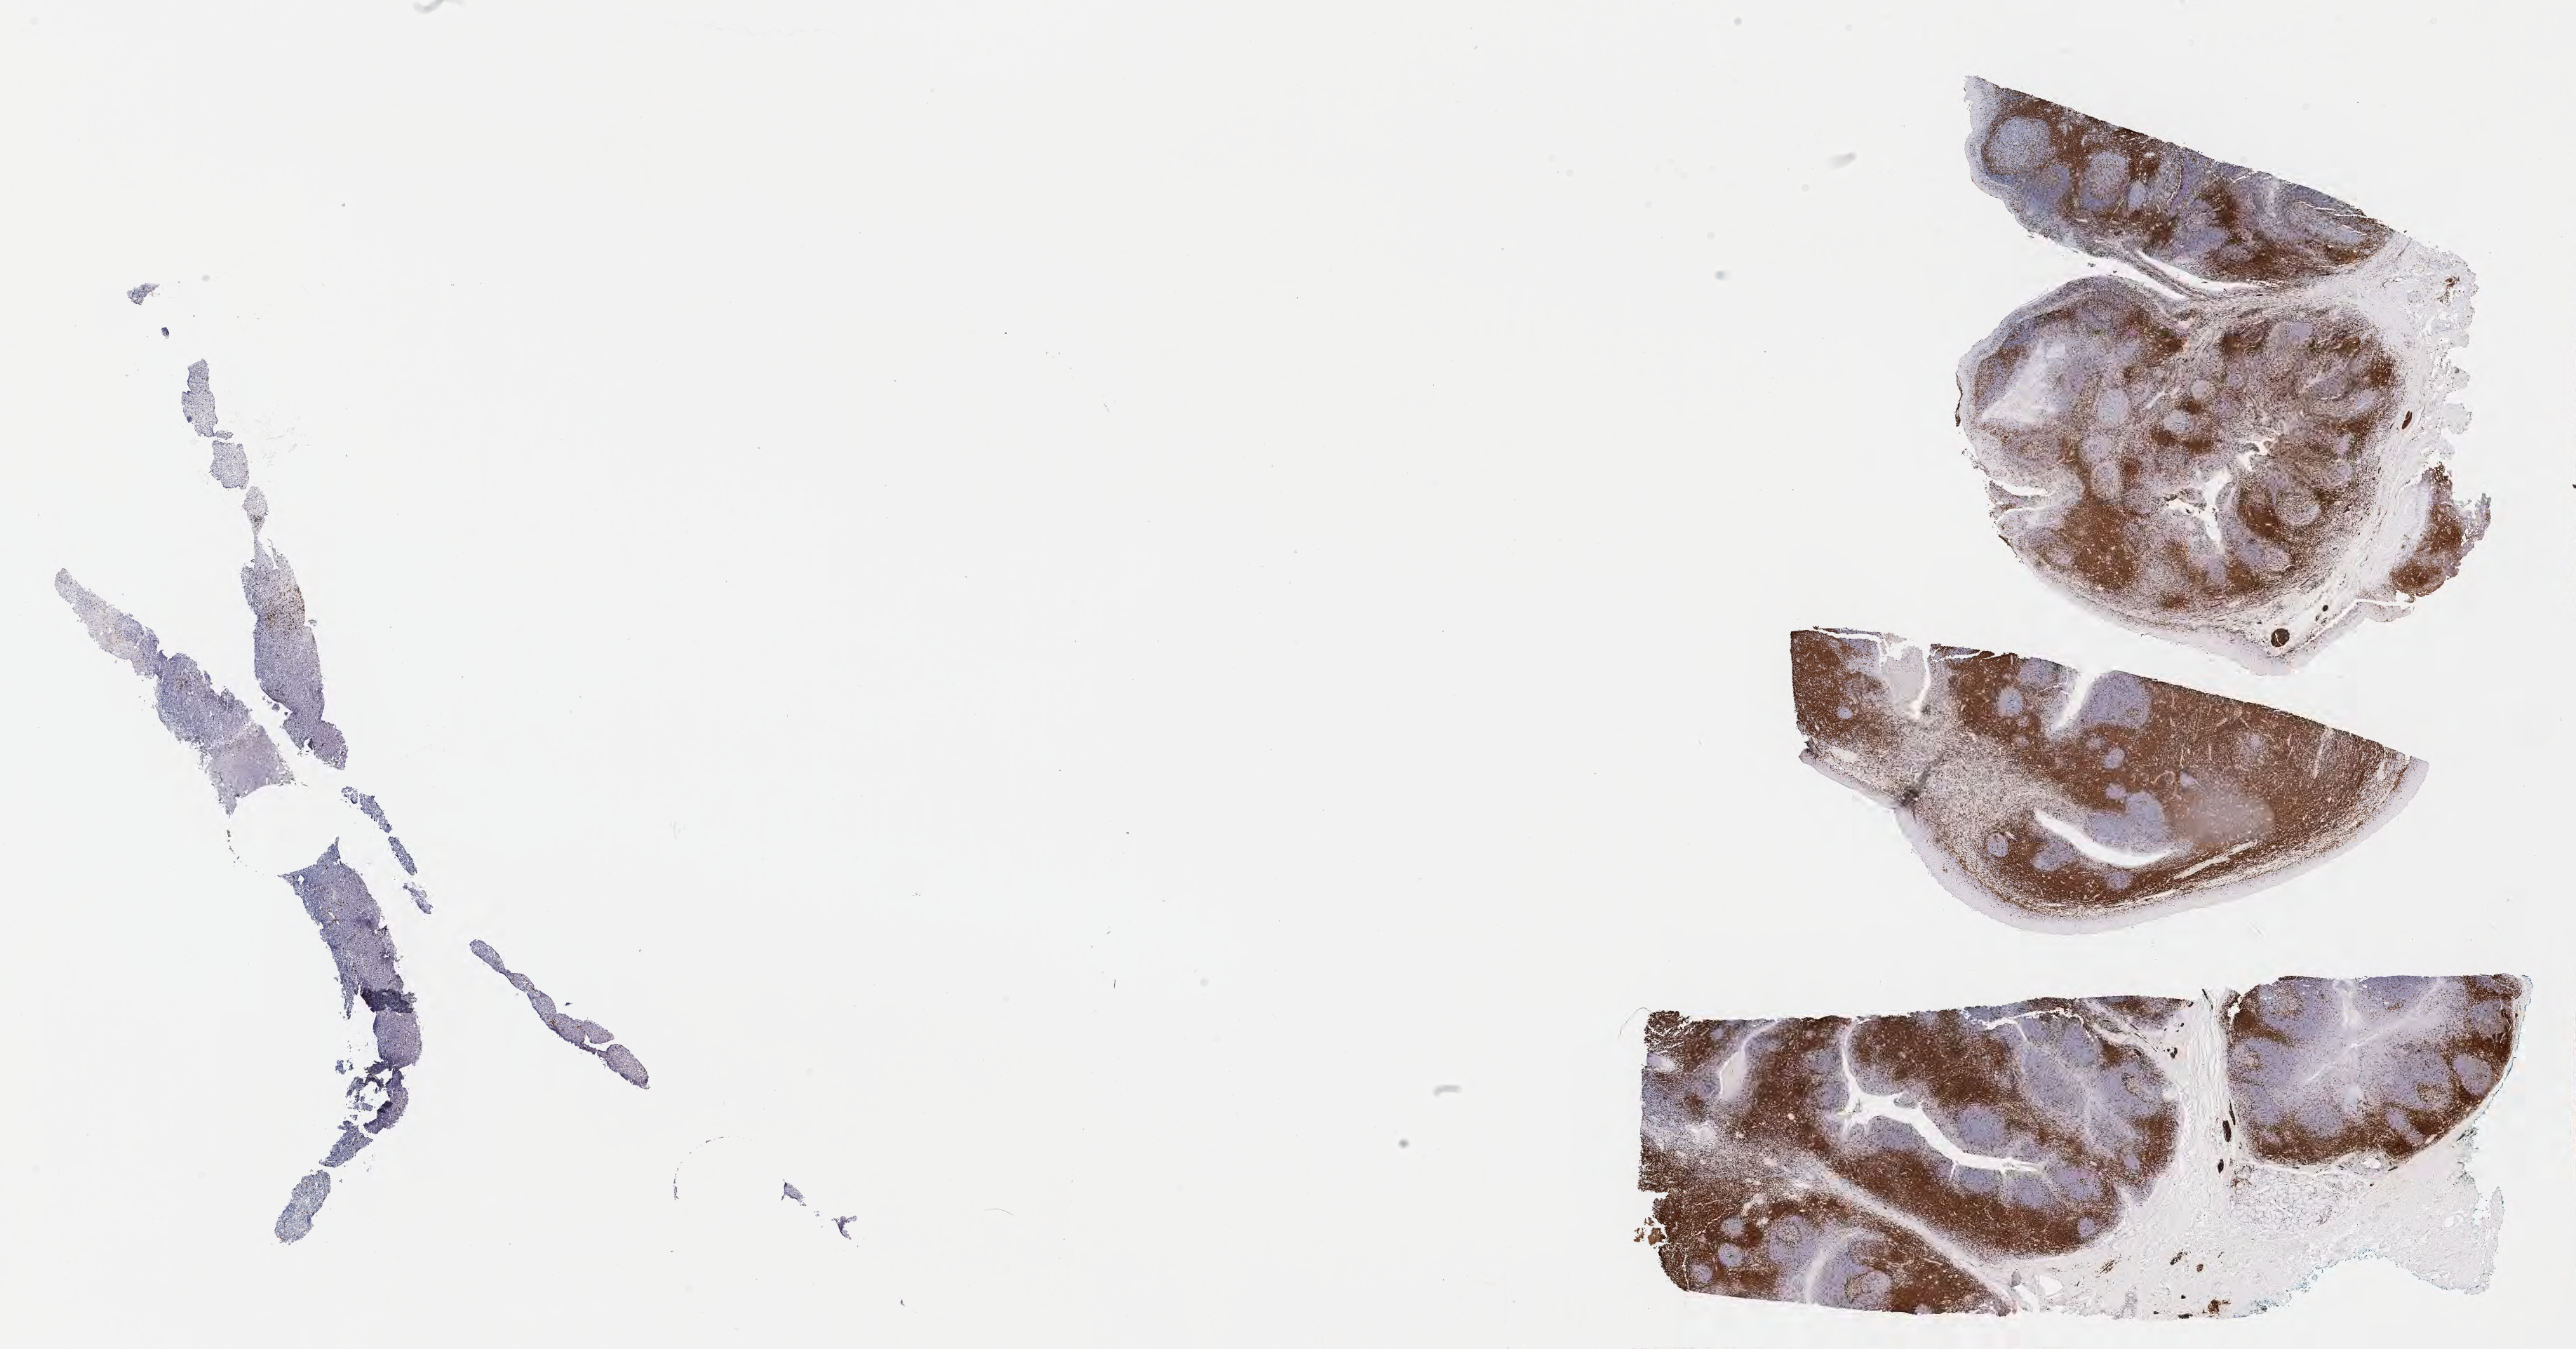
IHC for CD3, whole-slide image — a low-resolution overview of the entire scanned area, about 29.7 x 15.5 mm; specimen: tumor tissue; anatomic site: abdomen proper. Patient male; aged 14.
Histologic diagnosis: Burkitt lymphoma, NOS.